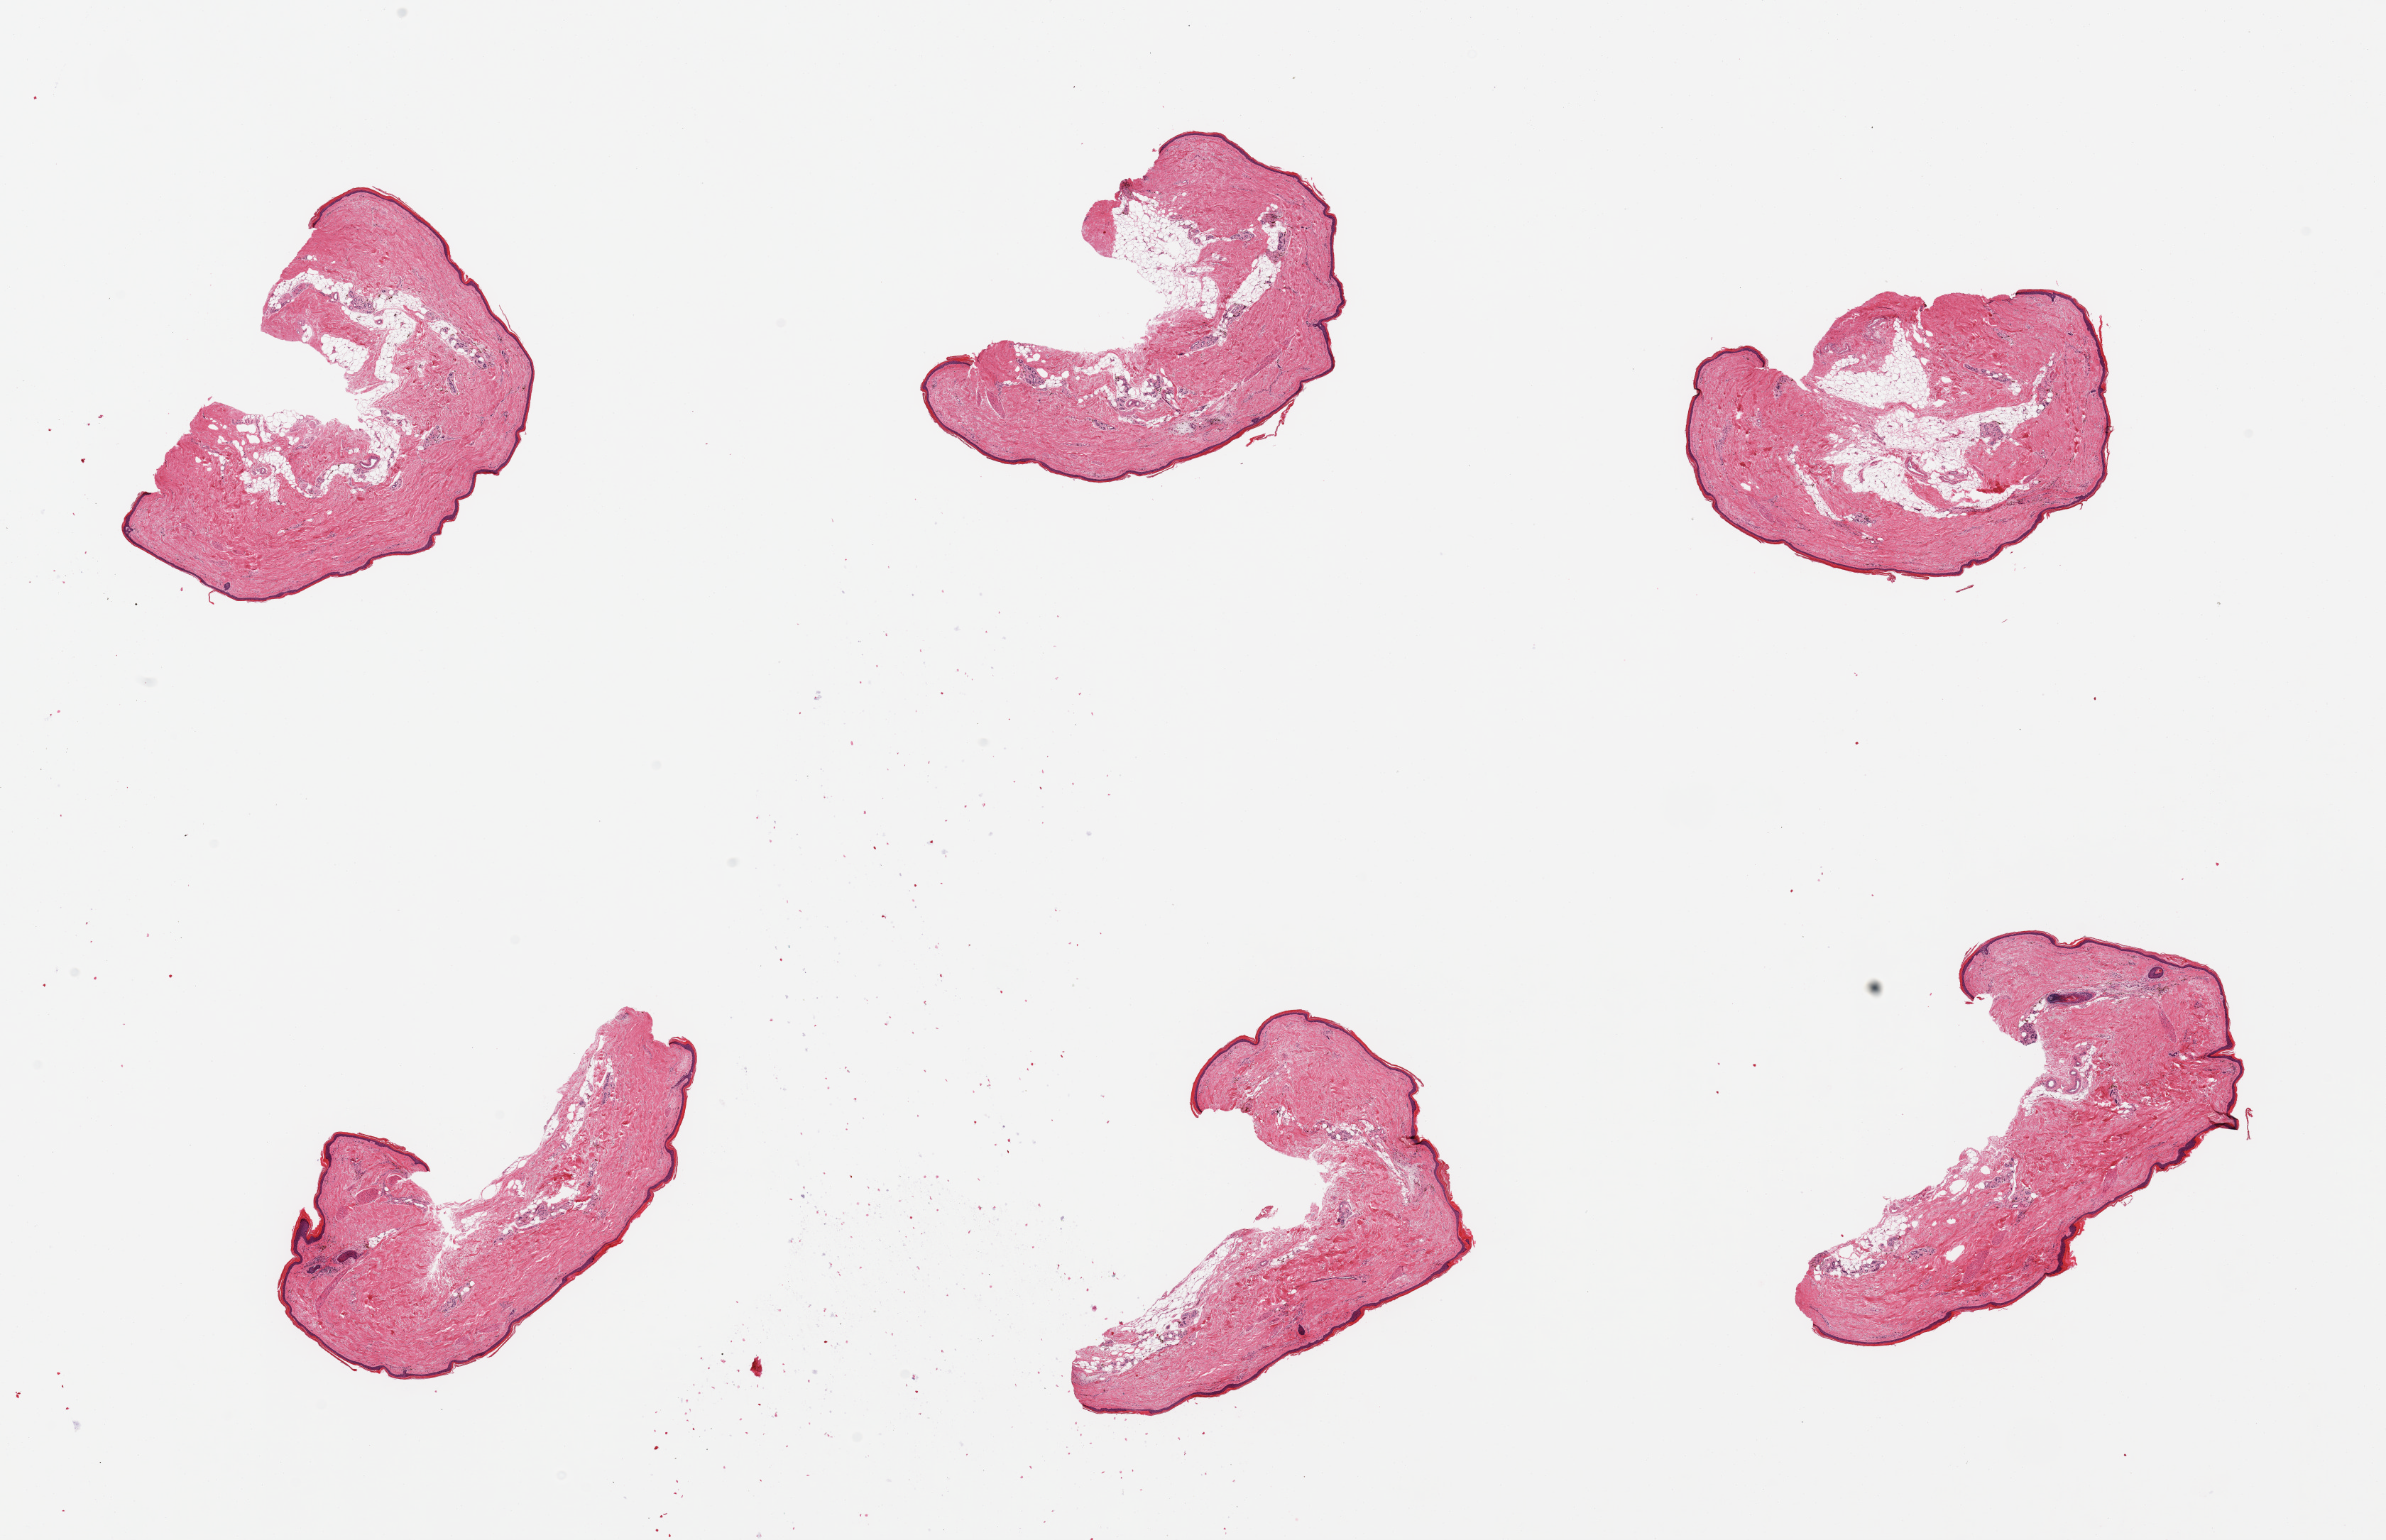
H&E whole-slide image, low-resolution overview of the scanned area, about 26.6 x 17.2 mm. PAXgene-fixed, paraffin-embedded tissue. Section of skin of lower leg (target tissue). Donor tissue sample. Donor sex: male.
Pathologist's review note for this sample: 6 pieces; includes up to 20% attached and internal fat, epidermis measures 23 microns.